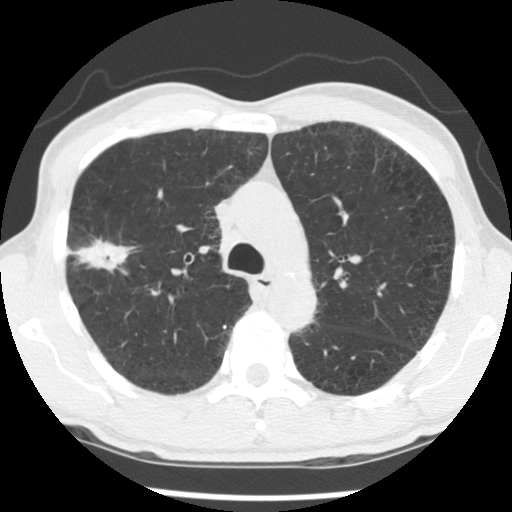
Low-dose screening chest CT, one axial slice; reconstruction kernel STANDARD; lung window (W 1500 / L -600 HU); 2.5 mm slice thickness; 512 × 512 image matrix.
Annotated regions visible in this slice (expert manual segmentation):
- lesion 1 (tumor, upper lobe of right lung): box from (x=73, y=238) to (x=135, y=273) px